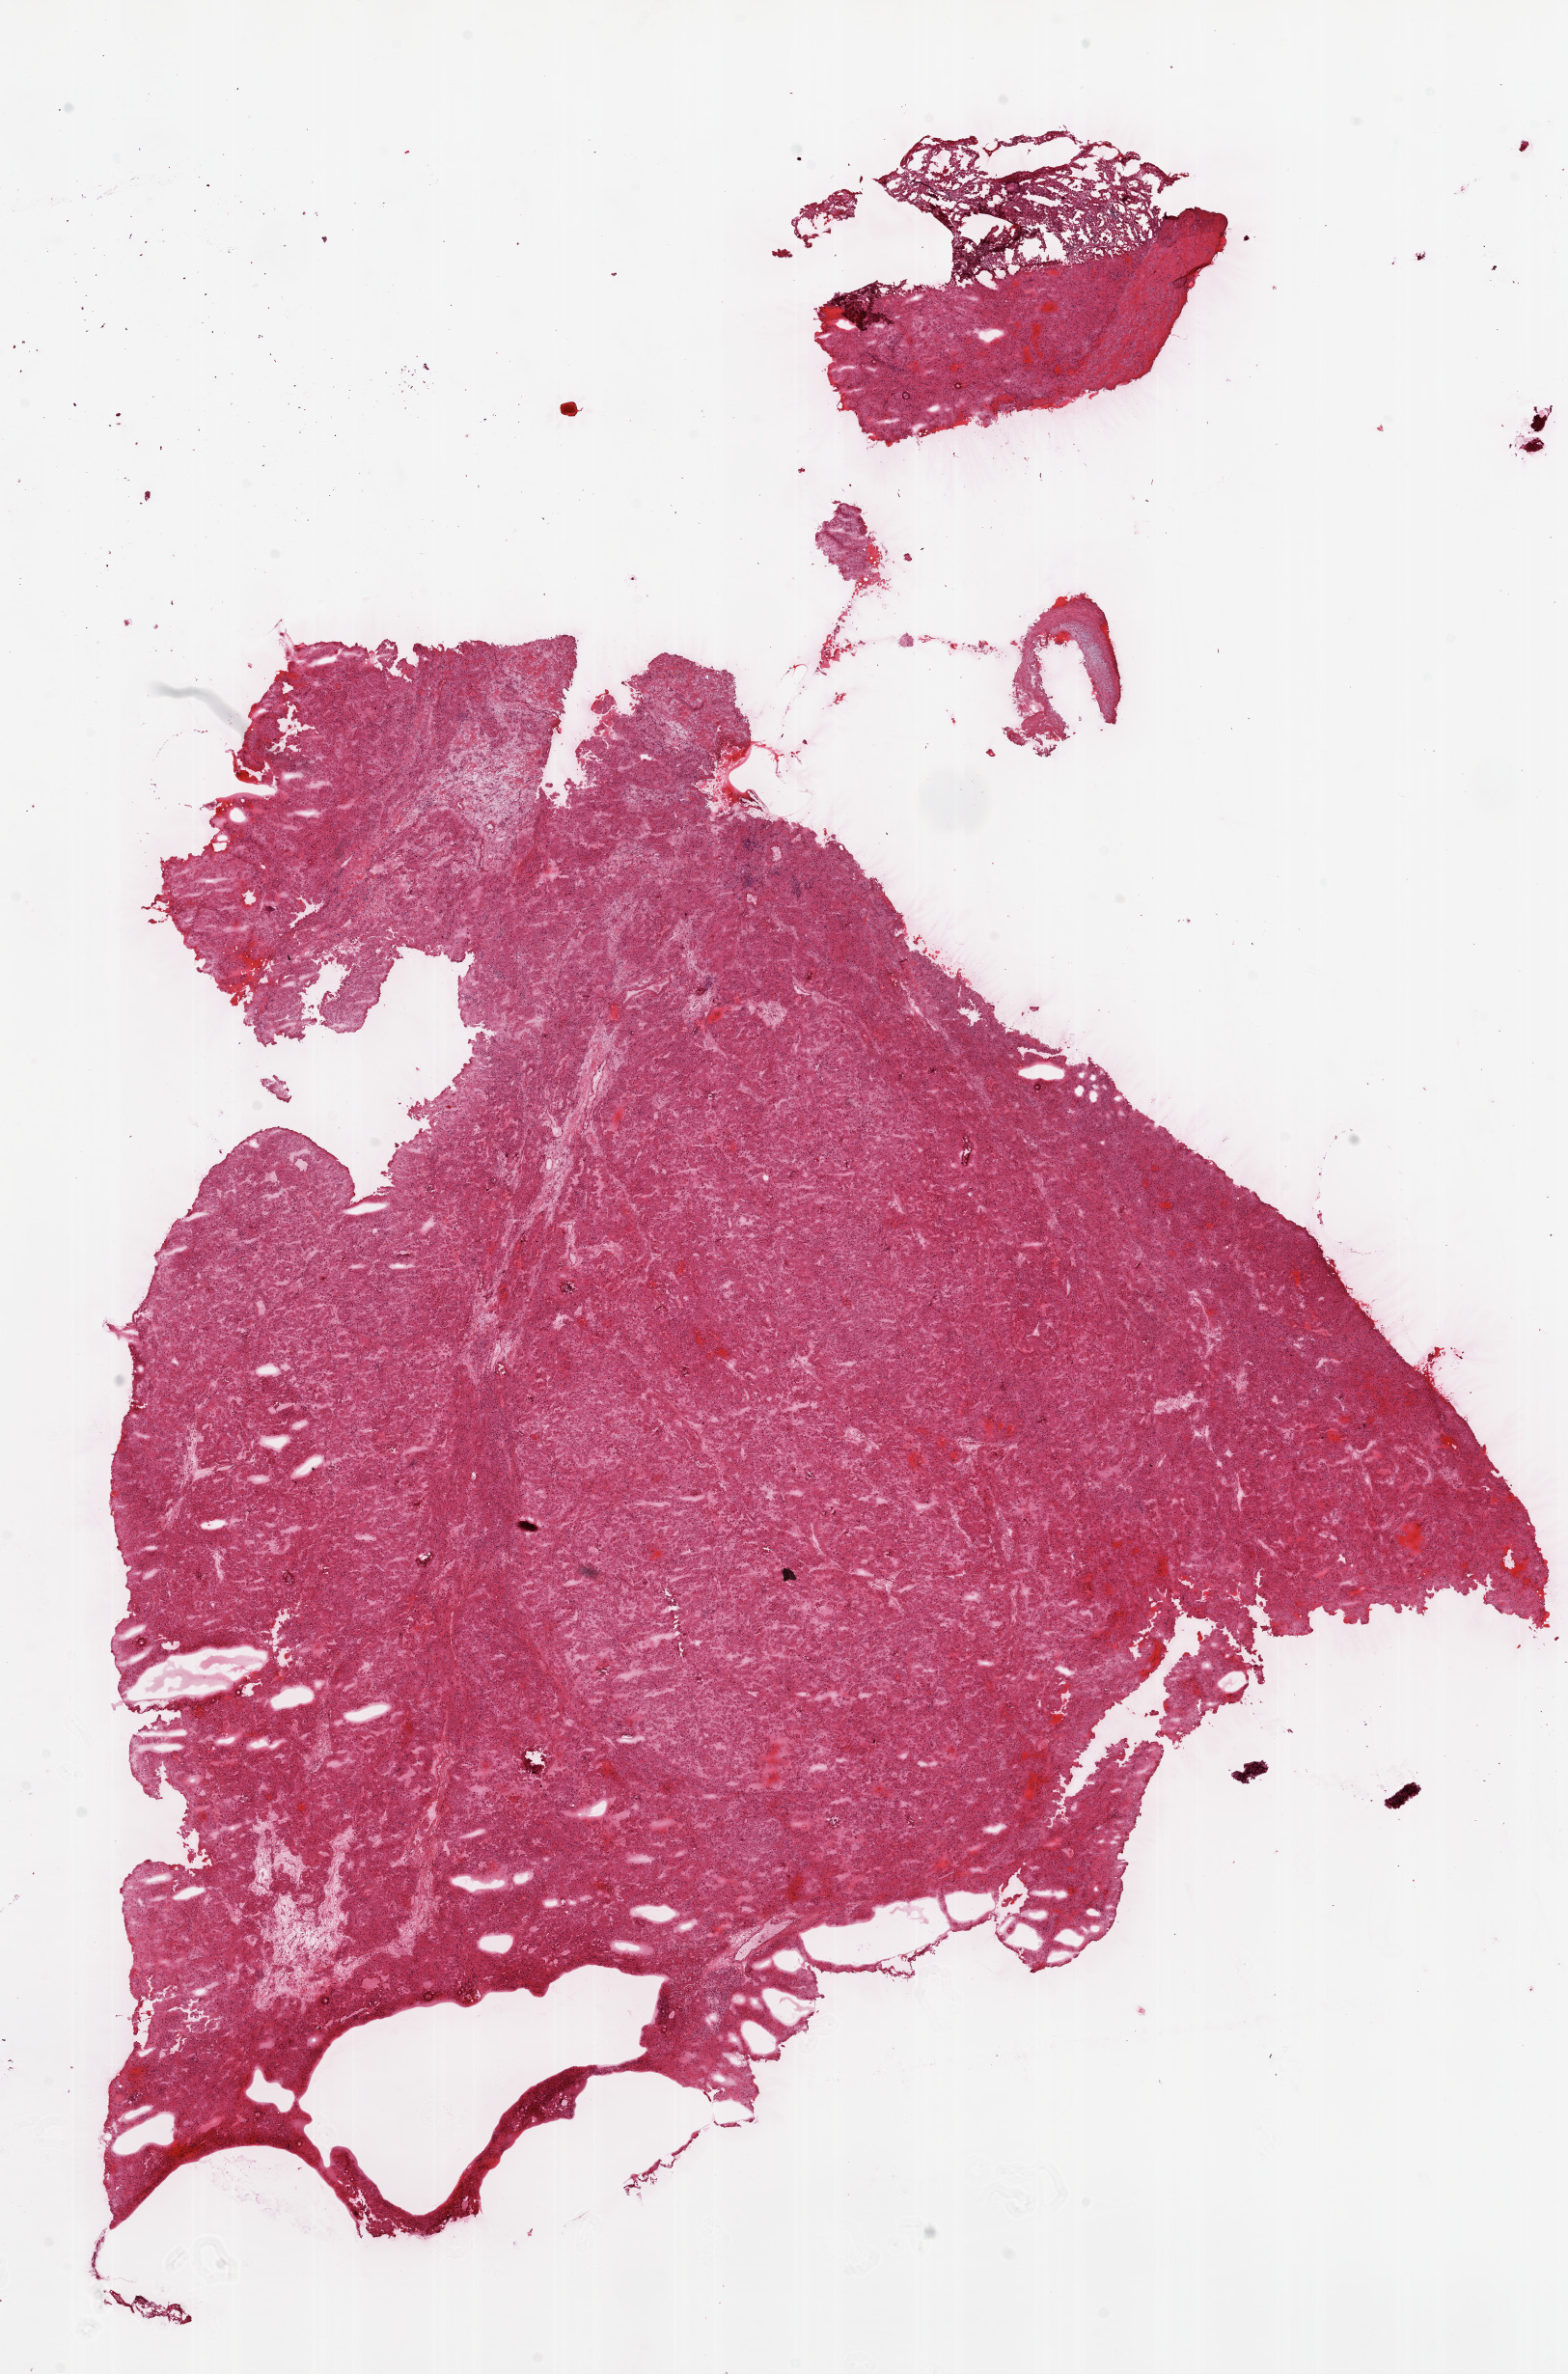
H&E whole-slide image — low-resolution overview of the scanned area, about 13.0 x 19.7 mm; frozen section; sample: primary tumour, kidney. Male patient; age at initial diagnosis 61 years. Histologic grade: G3 (poorly differentiated). Composition of this section per pathologist review: tumour cells 95%, tumour nuclei 90%, normal cells 0%, stromal cells 5%, necrosis 0%.
TNM: T1a NX M0. AJCC pathologic stage: I. Histologic diagnosis: Clear cell adenocarcinoma, NOS.